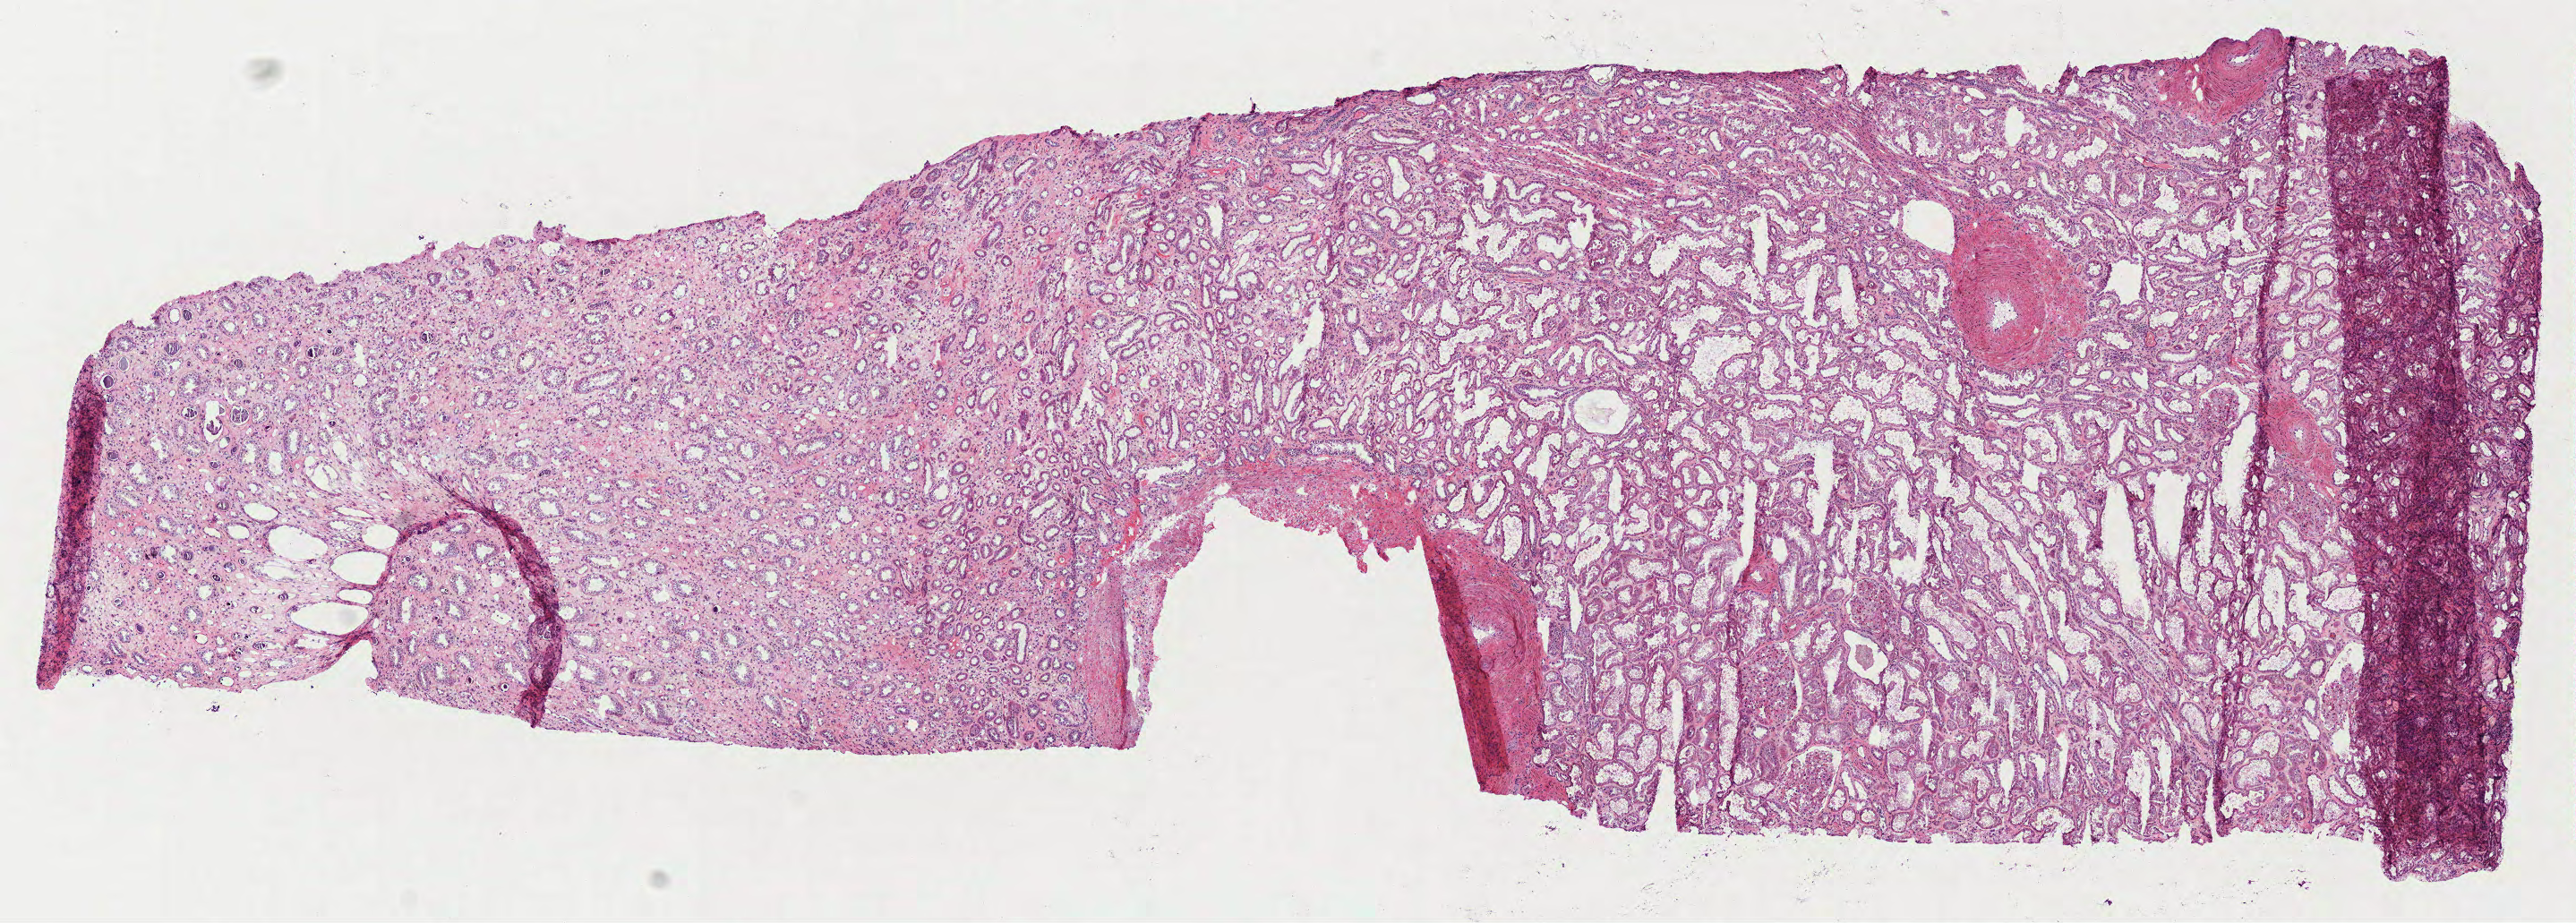
H&E-stained whole-slide image, shown as a low-resolution overview of the whole scanned area (about 11.6 x 4.2 mm, slide scanned at 40x), frozen section from the top of the tissue portion, kidney, solid tissue normal (non-tumour tissue) sample. Patient: male, age at initial diagnosis 63 years.
This section: solid tissue normal (non-tumour) sample from the same patient. Patient diagnosis: Papillary adenocarcinoma, NOS.